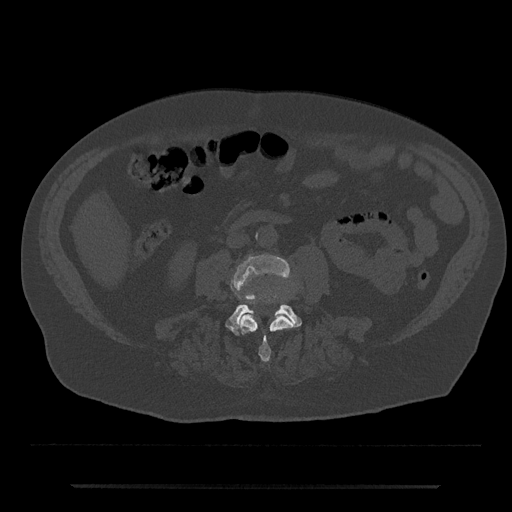
CT including the spine, one axial slice; slice 380 of 797 in the series (ordered by position); reconstruction kernel Br40s/3; 120 kVp; bone window (W 1800 / L 400 HU); 0.5 mm slice thickness; 512 × 512 image matrix, field of view 434 × 434 mm. Male patient, age 80 years. From the clinical record (not read from this slice): primary cancer: prostate.
Outlined on this slice (semi-automatically segmented with operator editing):
- L3 vertebra: bounding box <231,254,293,362> (left, top, right, bottom; pixels)
- L4 vertebra: <225,295,302,335>